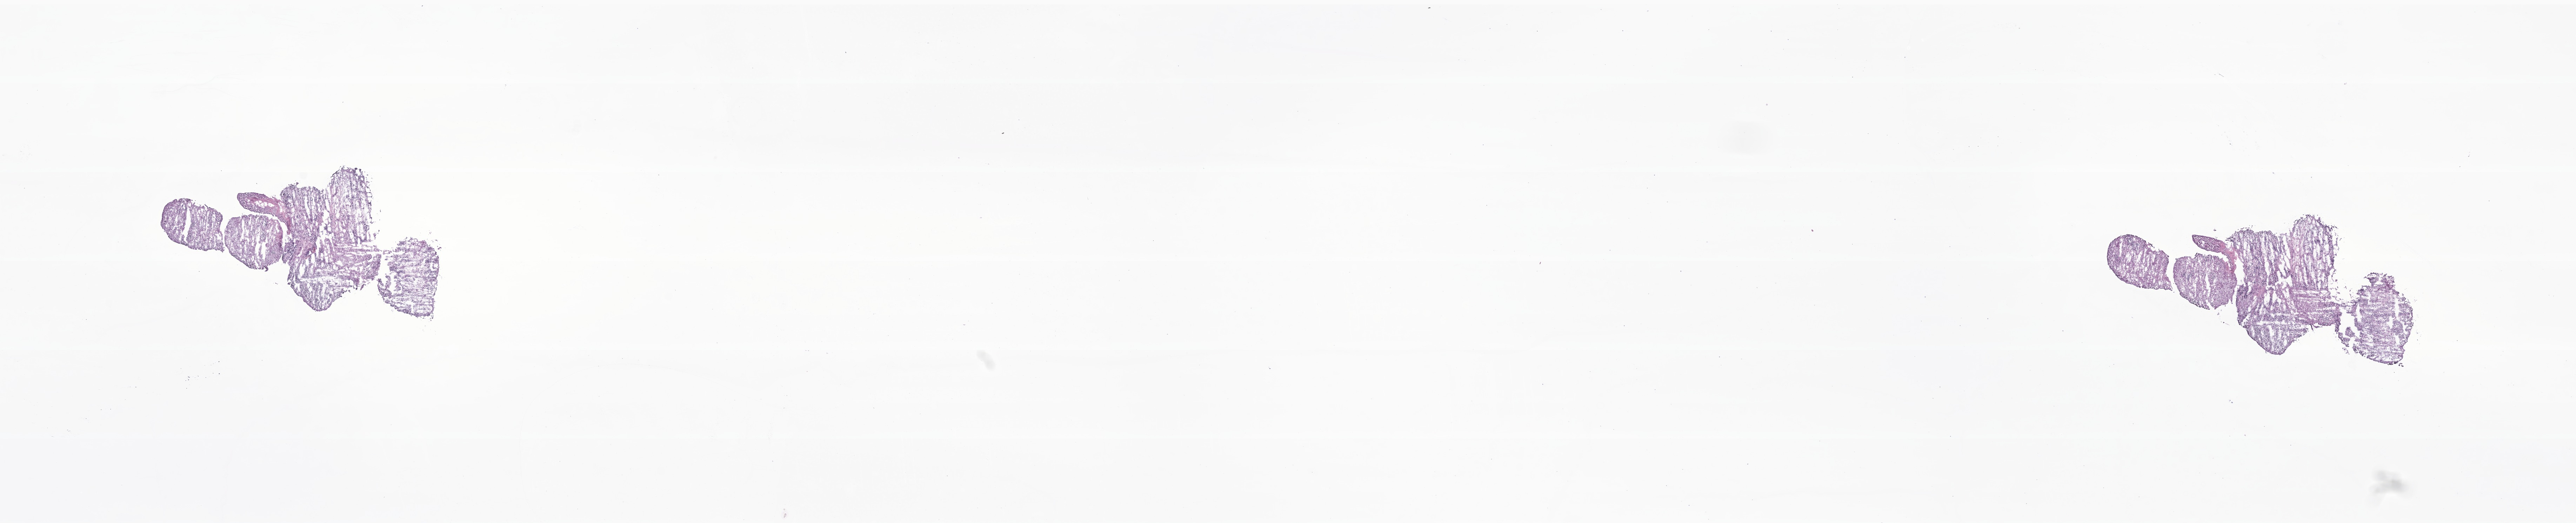
Whole-slide image, H&E stain of tumor tissue from the liver — shown as a low-resolution overview of the whole scanned area (about 31.0 x 6.3 mm). Frozen section (OCT-embedded). Patient male; age 156 days.
* recorded diagnosis: Neuroblastoma, NOS